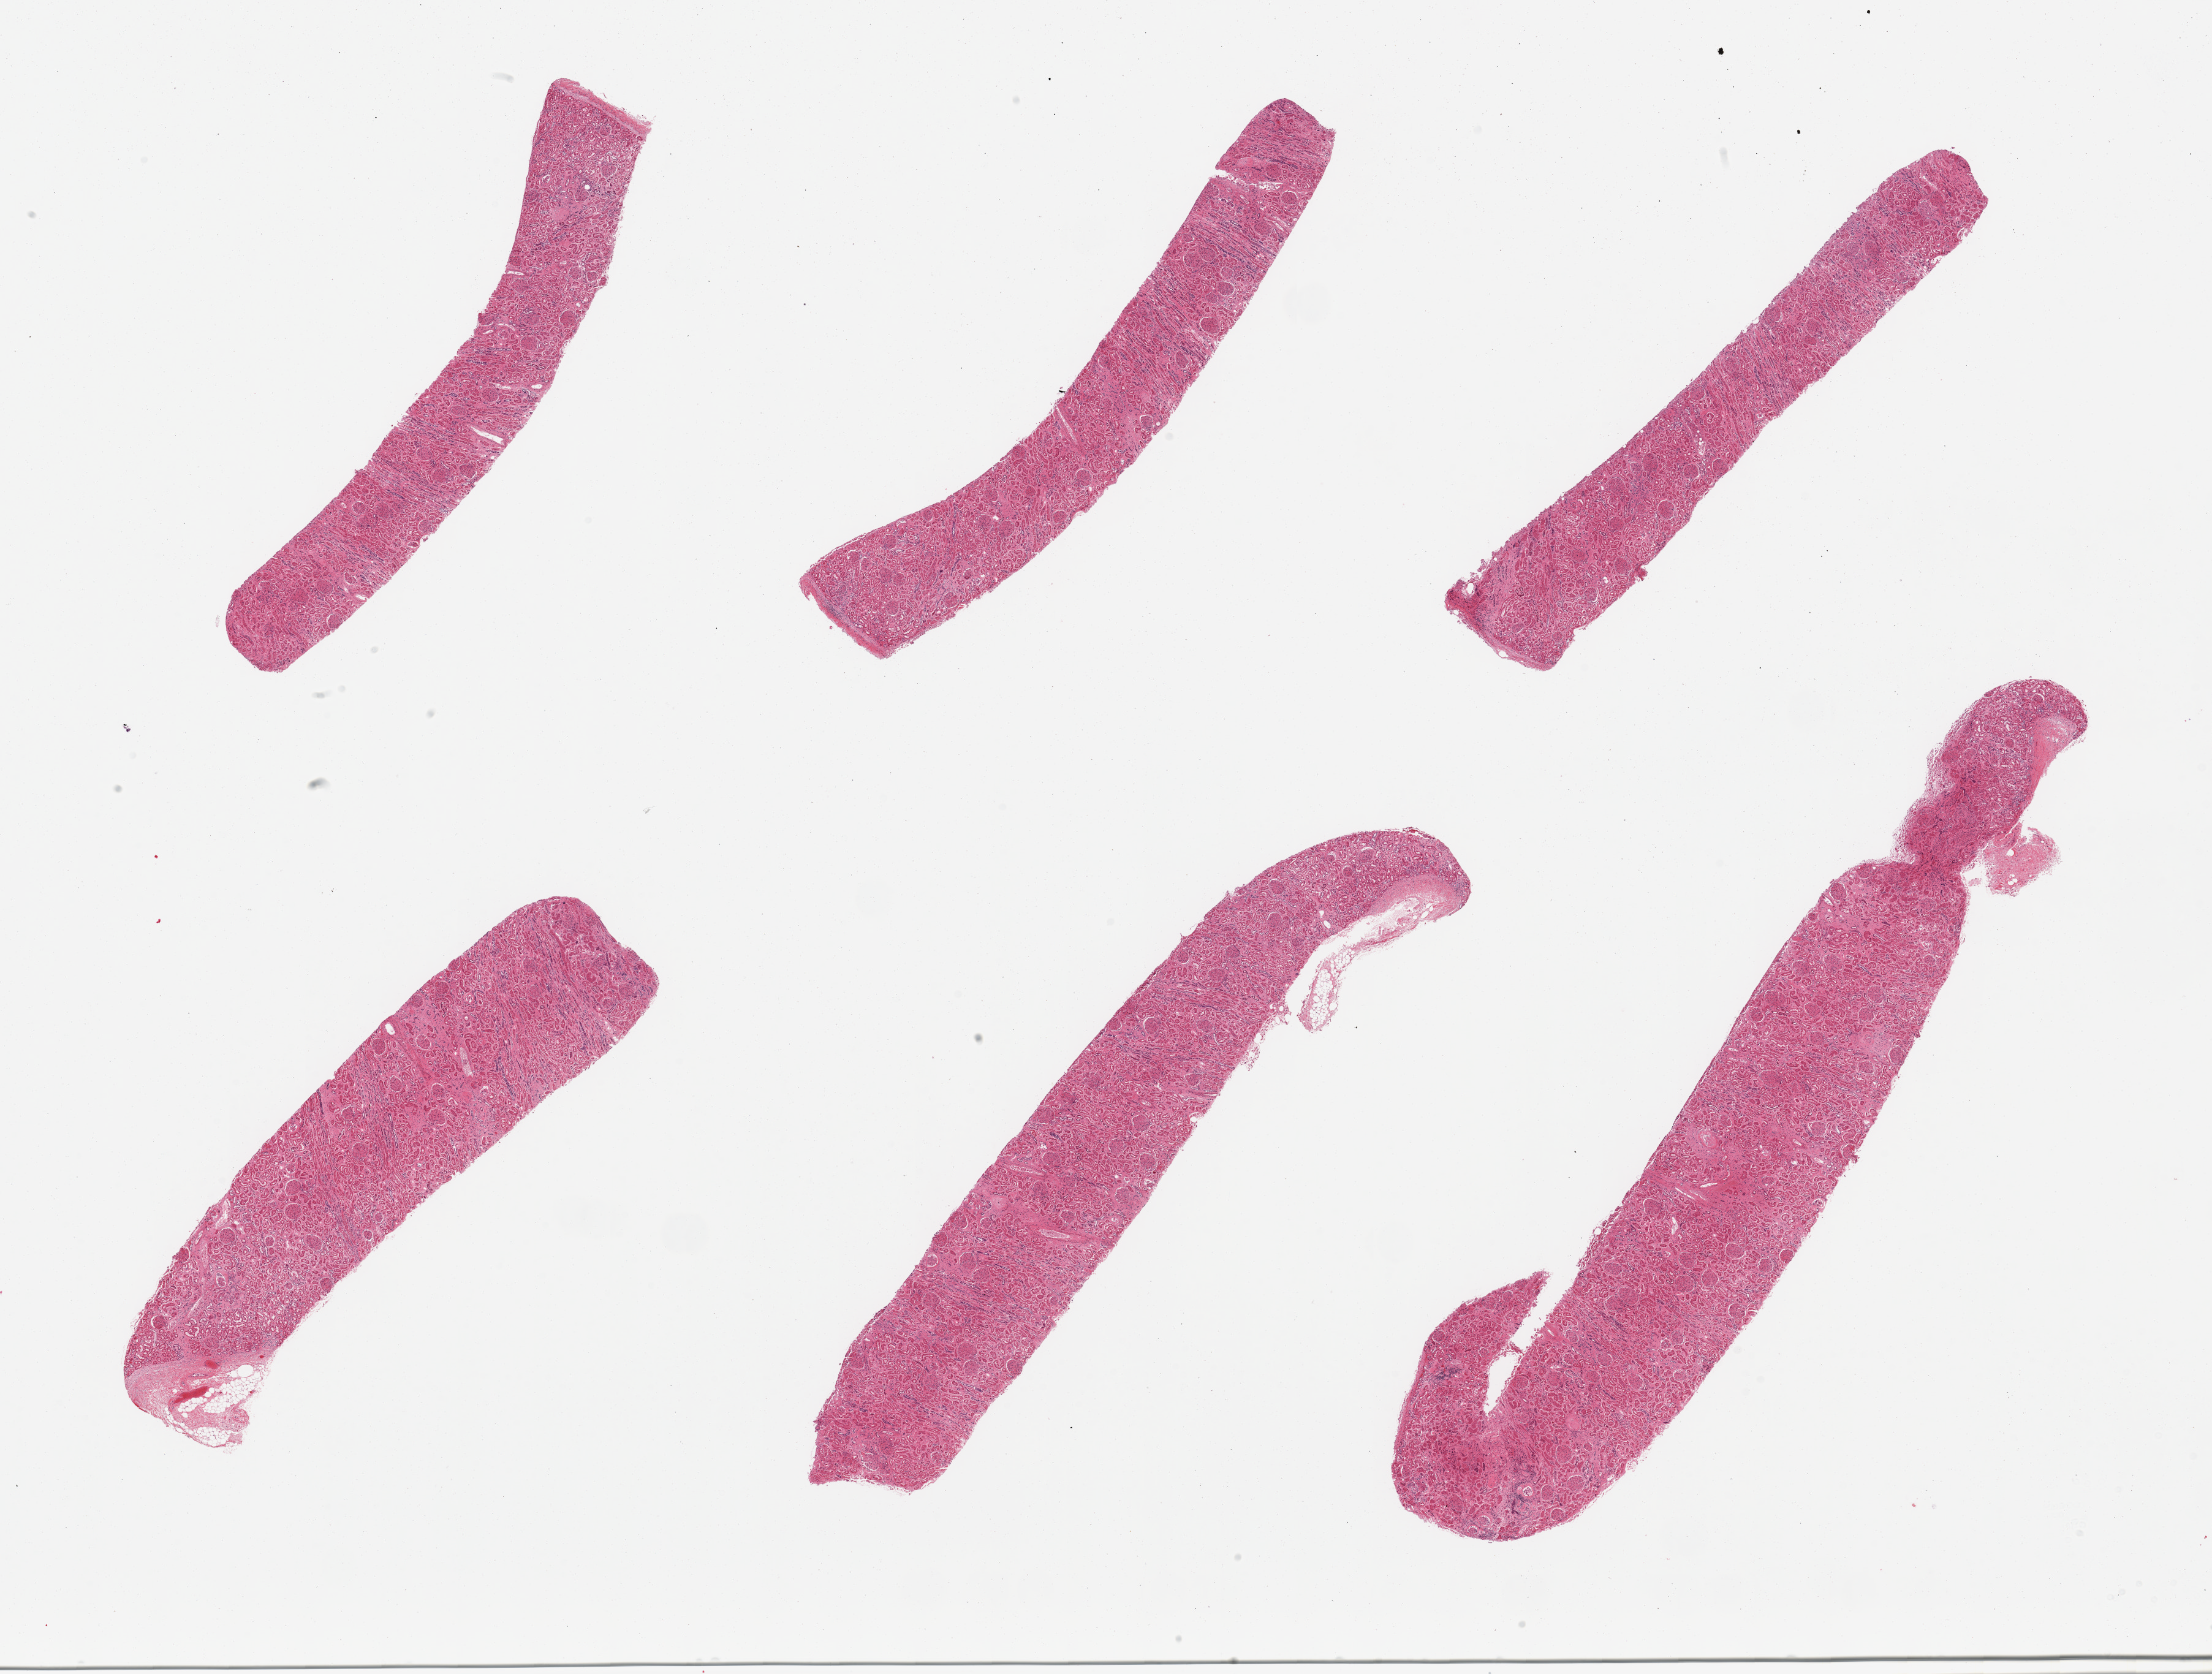
Digitized haematoxylin and eosin-stained section, brightfield — whole scanned area (about 28.5 x 21.6 mm) shown as a low-resolution overview; PAXgene-fixed, paraffin-embedded tissue; target tissue: renal cortex; tissue donor sample. Donor: male.
Reviewer comment on this tissue sample: 6 pieces; occasional scarred areas.